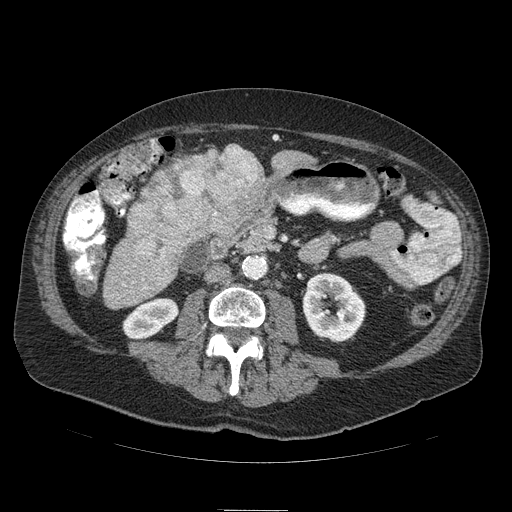
Contrast-enhanced abdominal CT (liver protocol), one axial slice; reconstruction kernel STANDARD; 120 kVp; soft-tissue window (W 400 / L 40 HU); 2.5 mm slice thickness; 512 × 512 image matrix, field of view 440 × 440 mm. From the clinical record (not read from this slice): diagnosis: hepatocellular carcinoma (patient treated with transarterial chemoembolisation; whether this scan precedes or follows treatment is not stated here); TNM stage (as recorded): Stage-IIIA; Child-Pugh class: B; tumour differentiation: well differentiated; tumour nodularity: multinodular.
Structures marked on this image (semi-automatically segmented with operator editing):
- liver parenchyma outside the tumour (the mass and vessels are separate outlines, so this box may not span the whole liver): bounding box <124,144,312,242> (left, top, right, bottom; pixels)
- mass: <125,145,272,269>